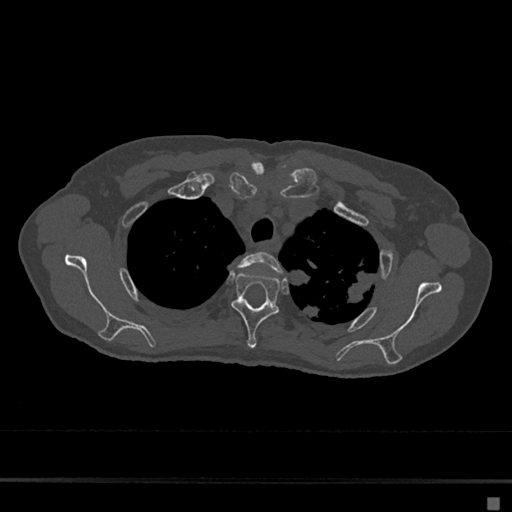
CT including the spine, one axial slice; slice 540 of 797 in the series (ordered by position); reconstruction kernel Br40s/3; bone window (W 1800 / L 400 HU); 0.5 mm slice thickness; 512 × 512 image matrix. Female patient, age 68 years. From the clinical record (not read from this slice): primary cancer: renal.
Outlined on this slice (semi-automatic segmentation, software-assisted and operator-edited):
- T2 vertebra: box from (x=237, y=252) to (x=283, y=273) px
- T3 vertebra: (x=231, y=272)–(x=280, y=349)